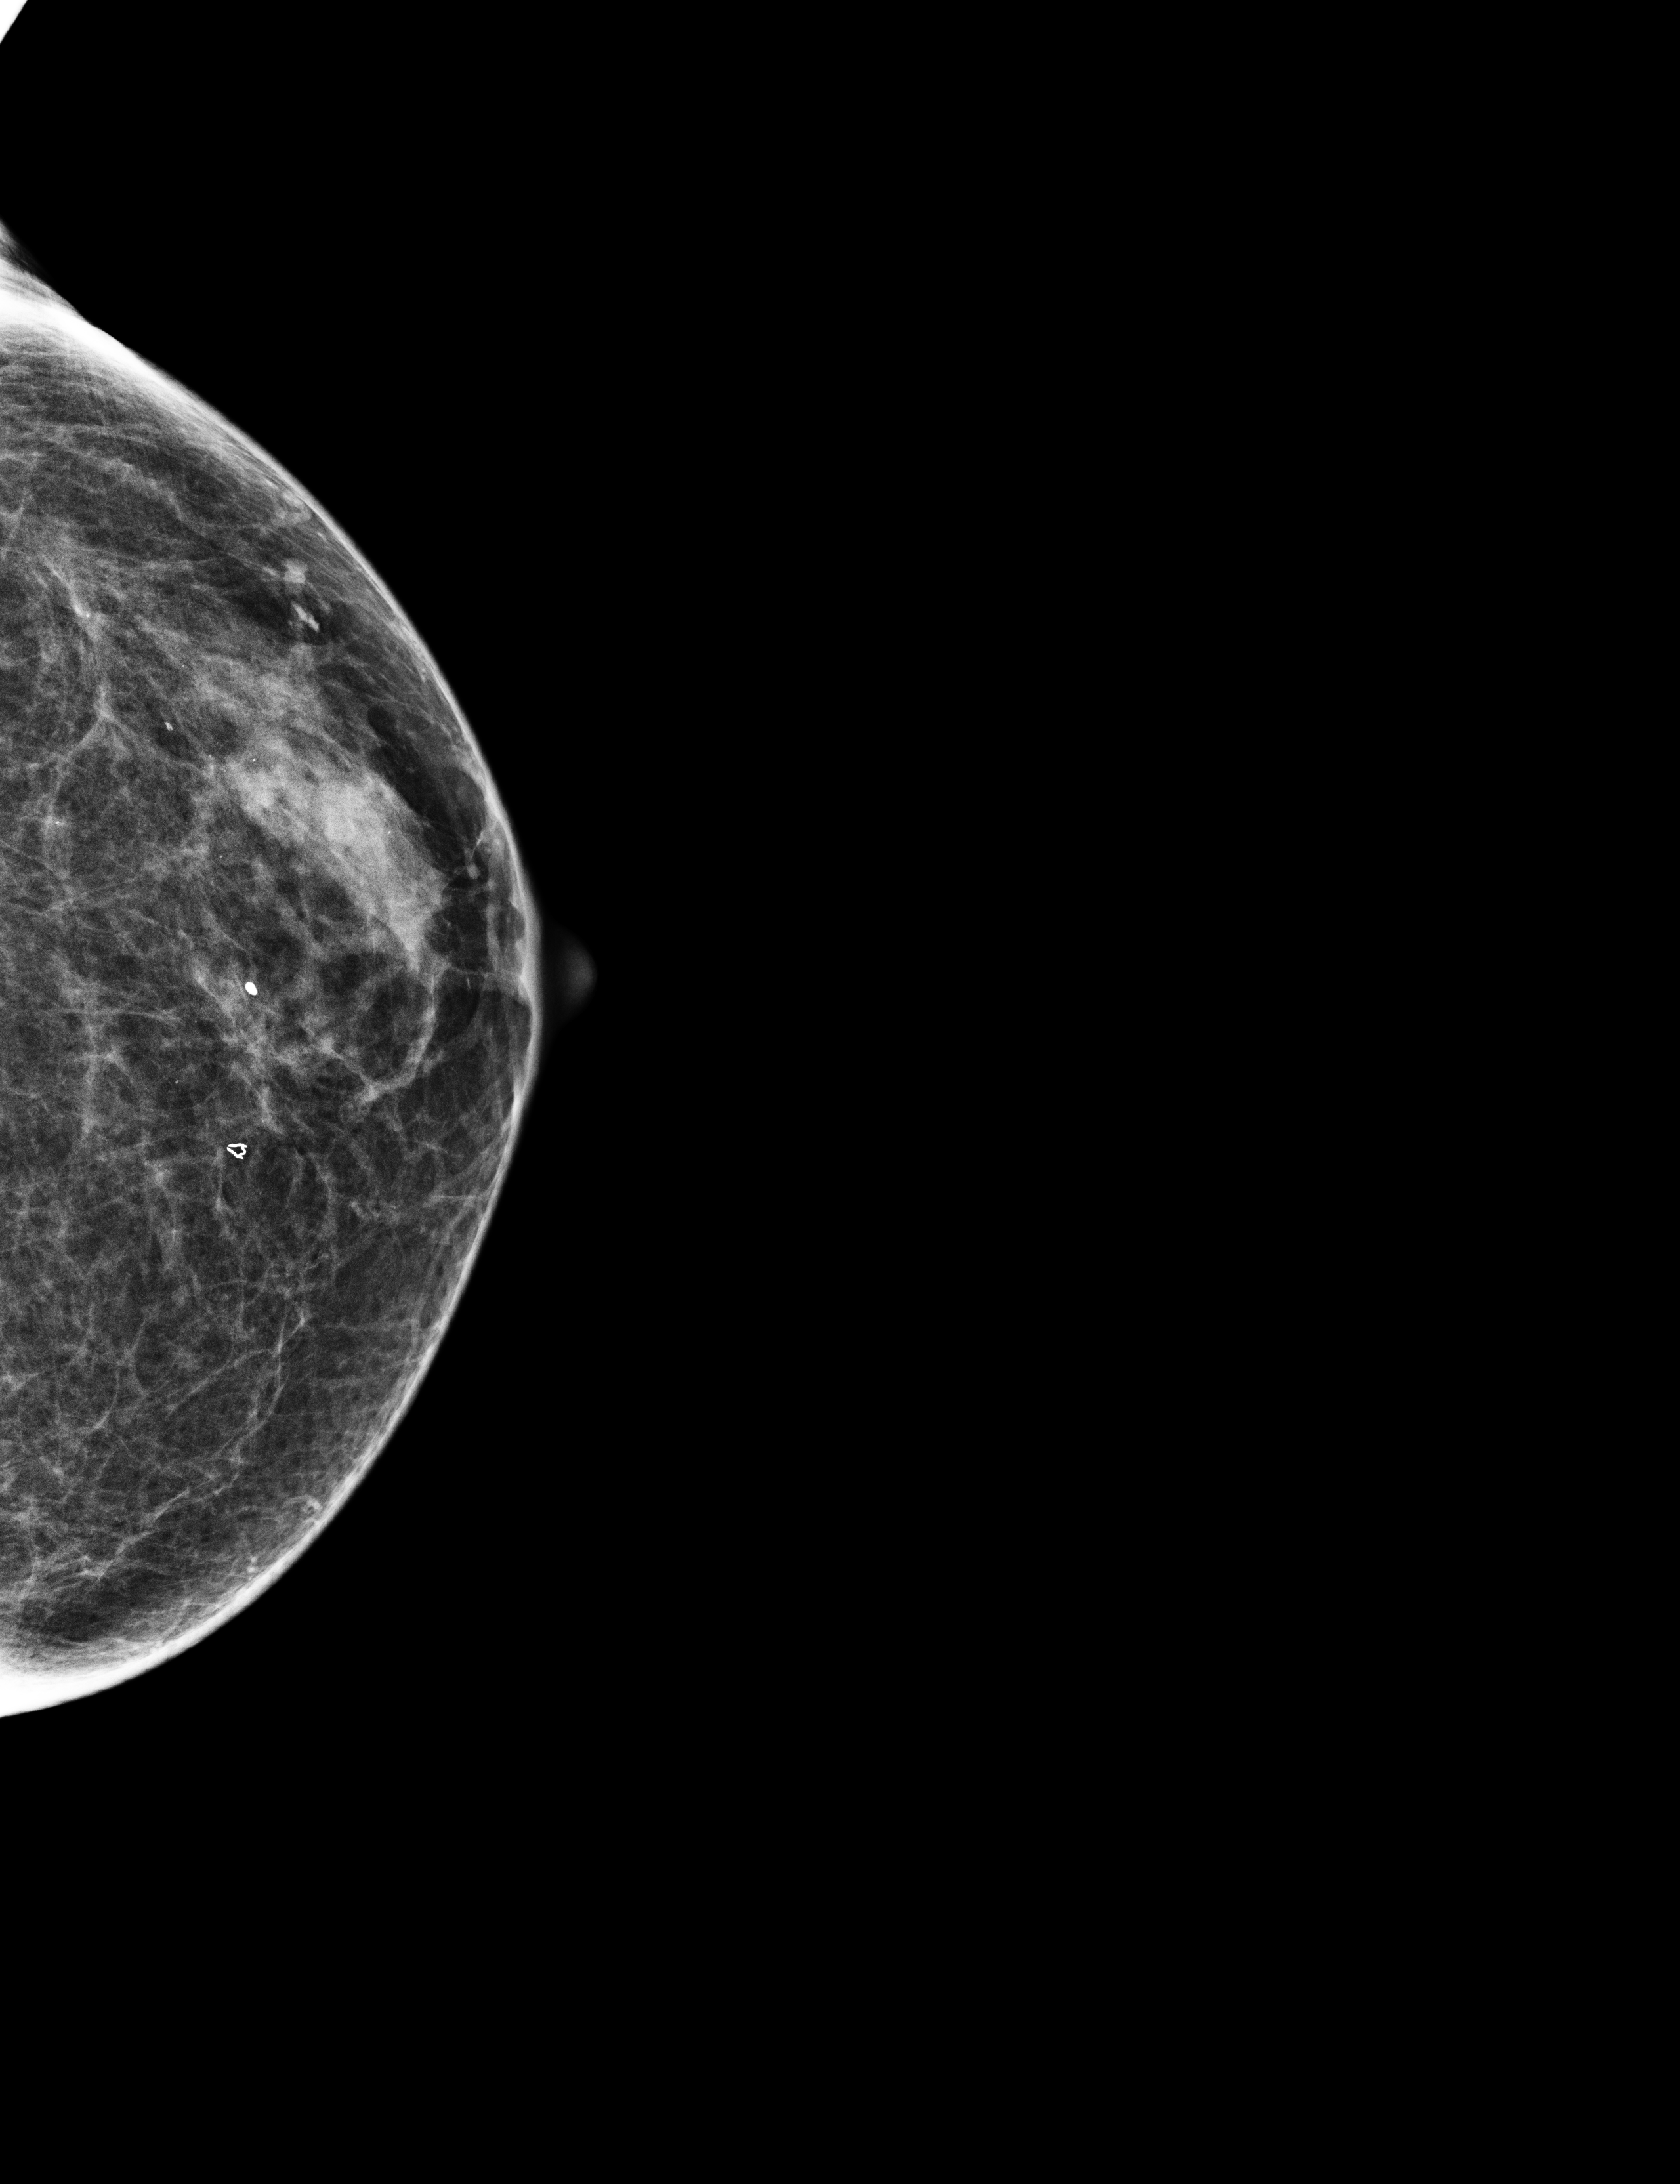
Digital mammogram (FFDM); left breast; craniocaudal (CC) view; annual screening mammography examination; compressed breast thickness 52 mm; system: Selenia Dimensions. Patient: female, 67 years.
Final BI-RADS category for the screening round (tomosynthesis exam, both breasts): category 2.